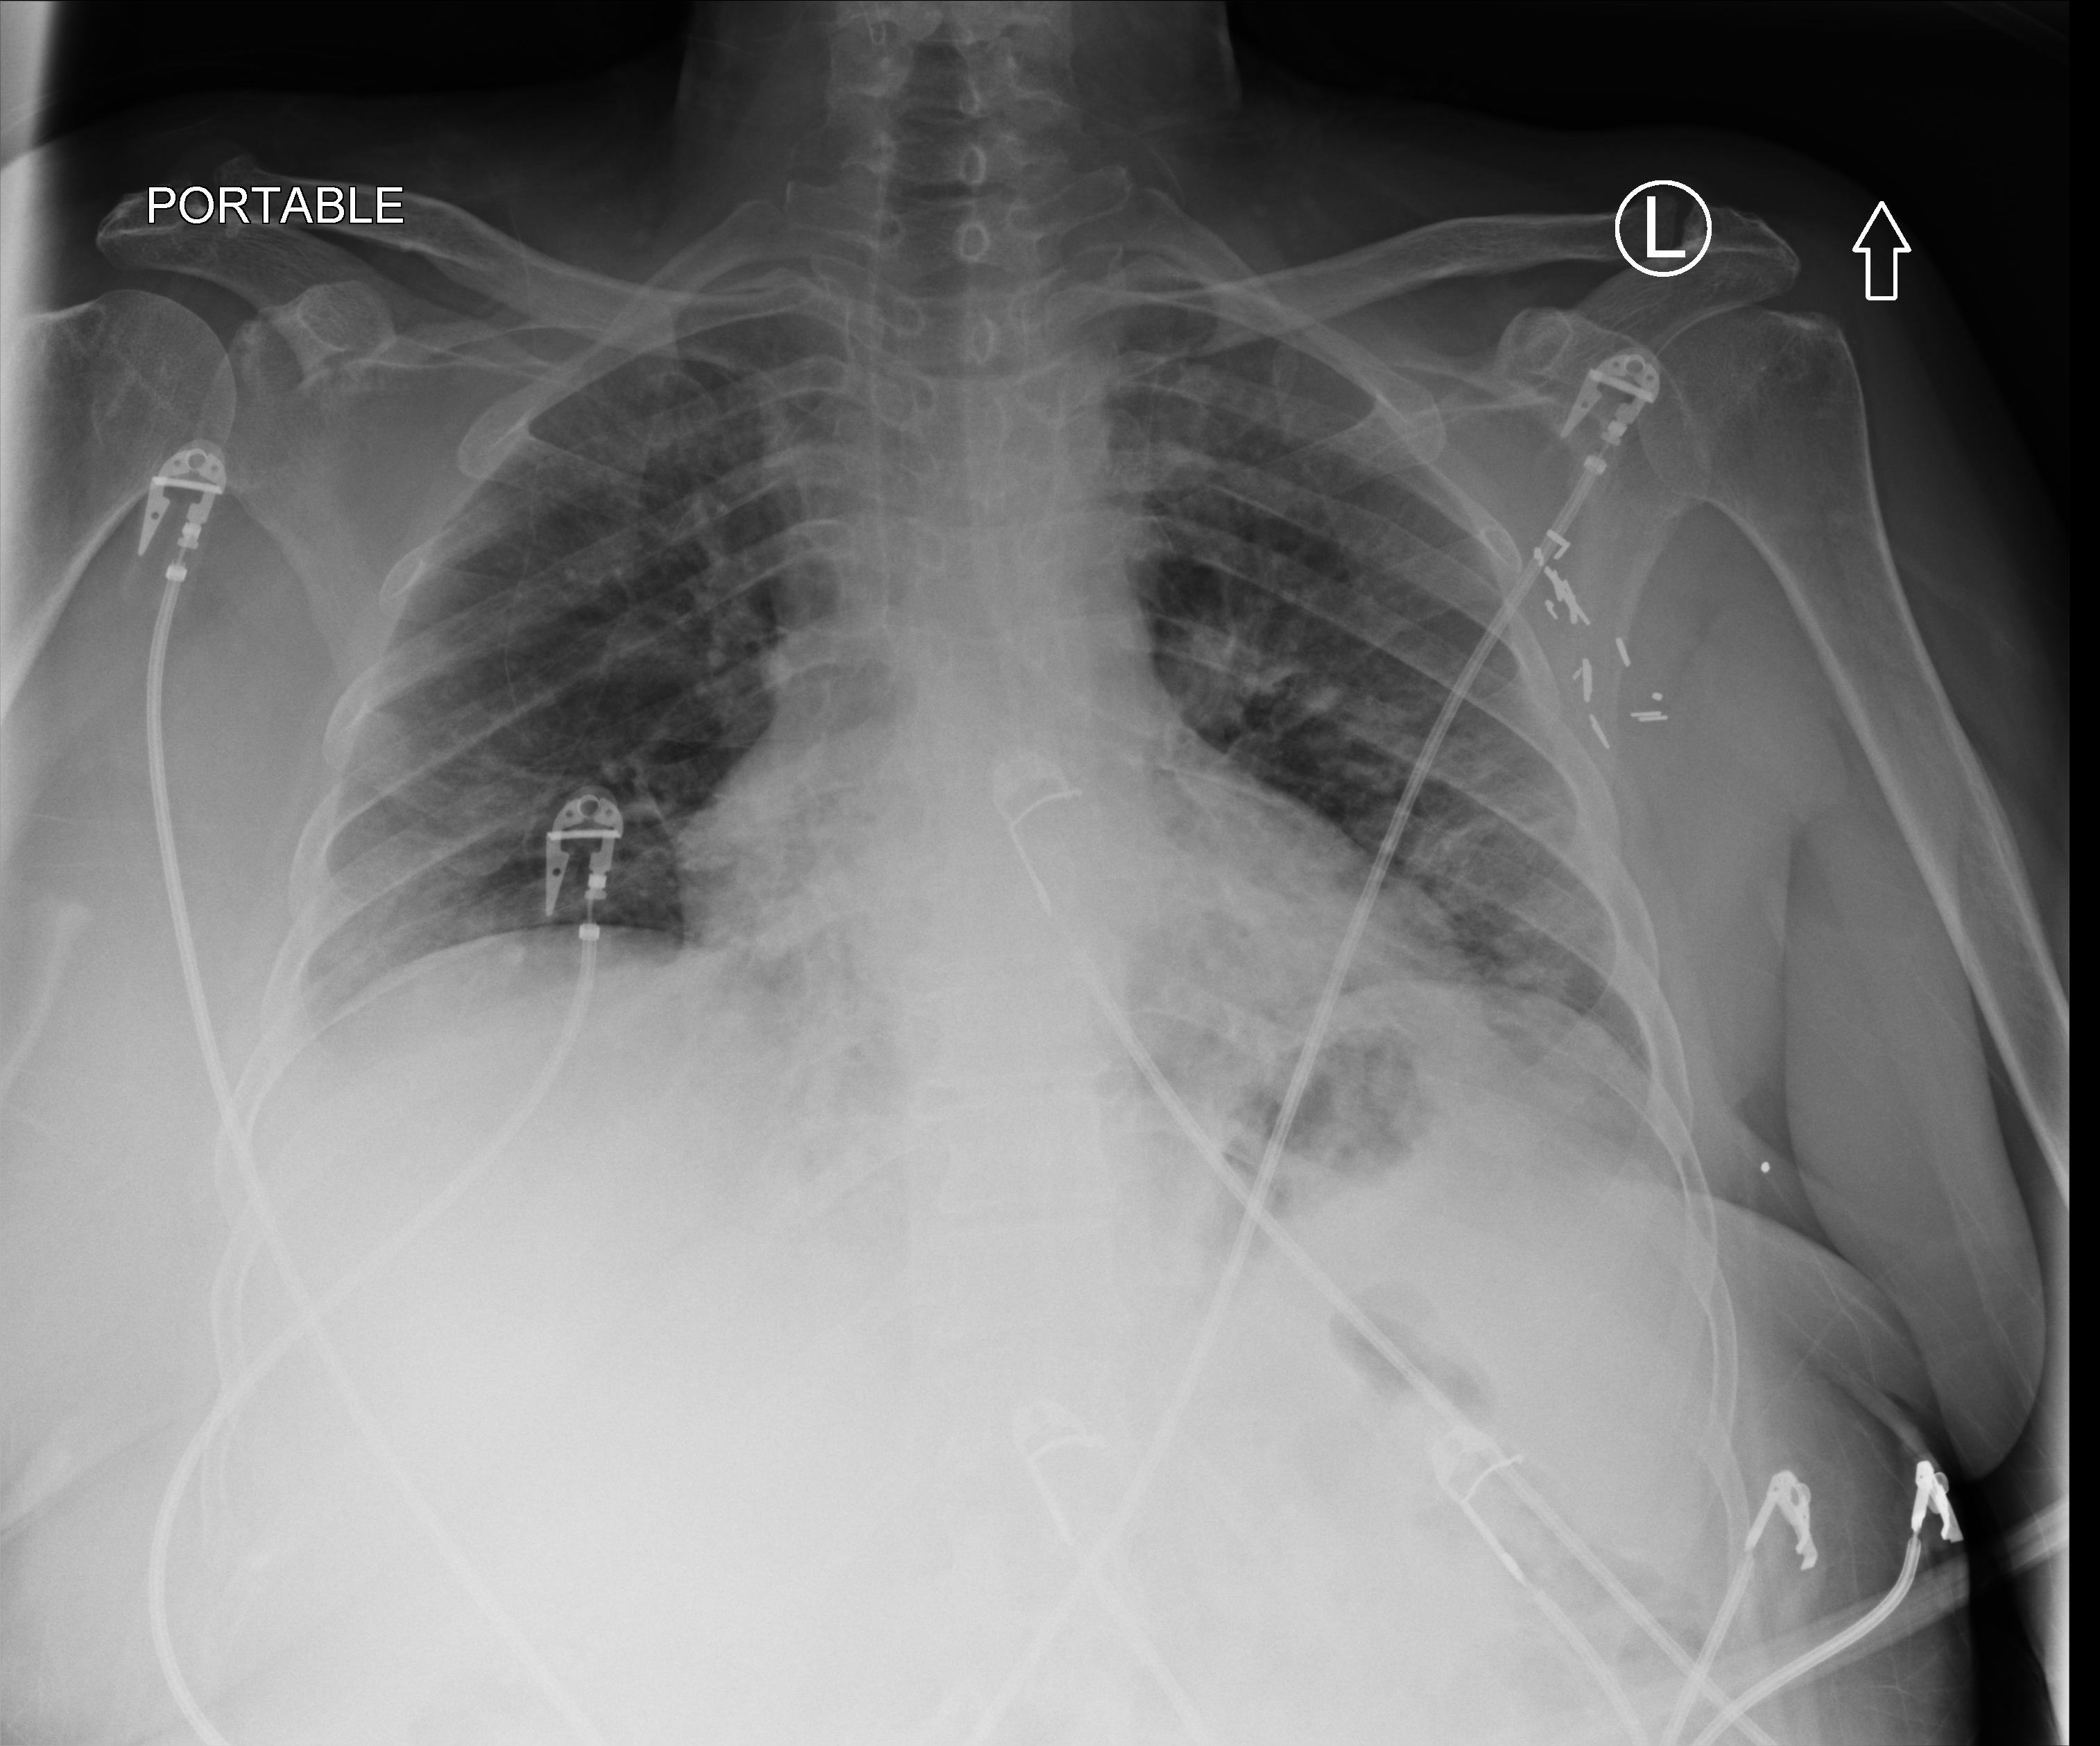
Bedside chest radiograph (computed radiography), anteroposterior (AP) projection. Female patient hospitalised with COVID-19, age 60–74 years.
From the hospital-stay record, not from the radiograph (when in the stay this image was taken is not recorded):
- mechanically ventilated during this hospital stay: yes
- length of hospital stay: 16 days
- admitted to intensive care during this hospital stay: yes